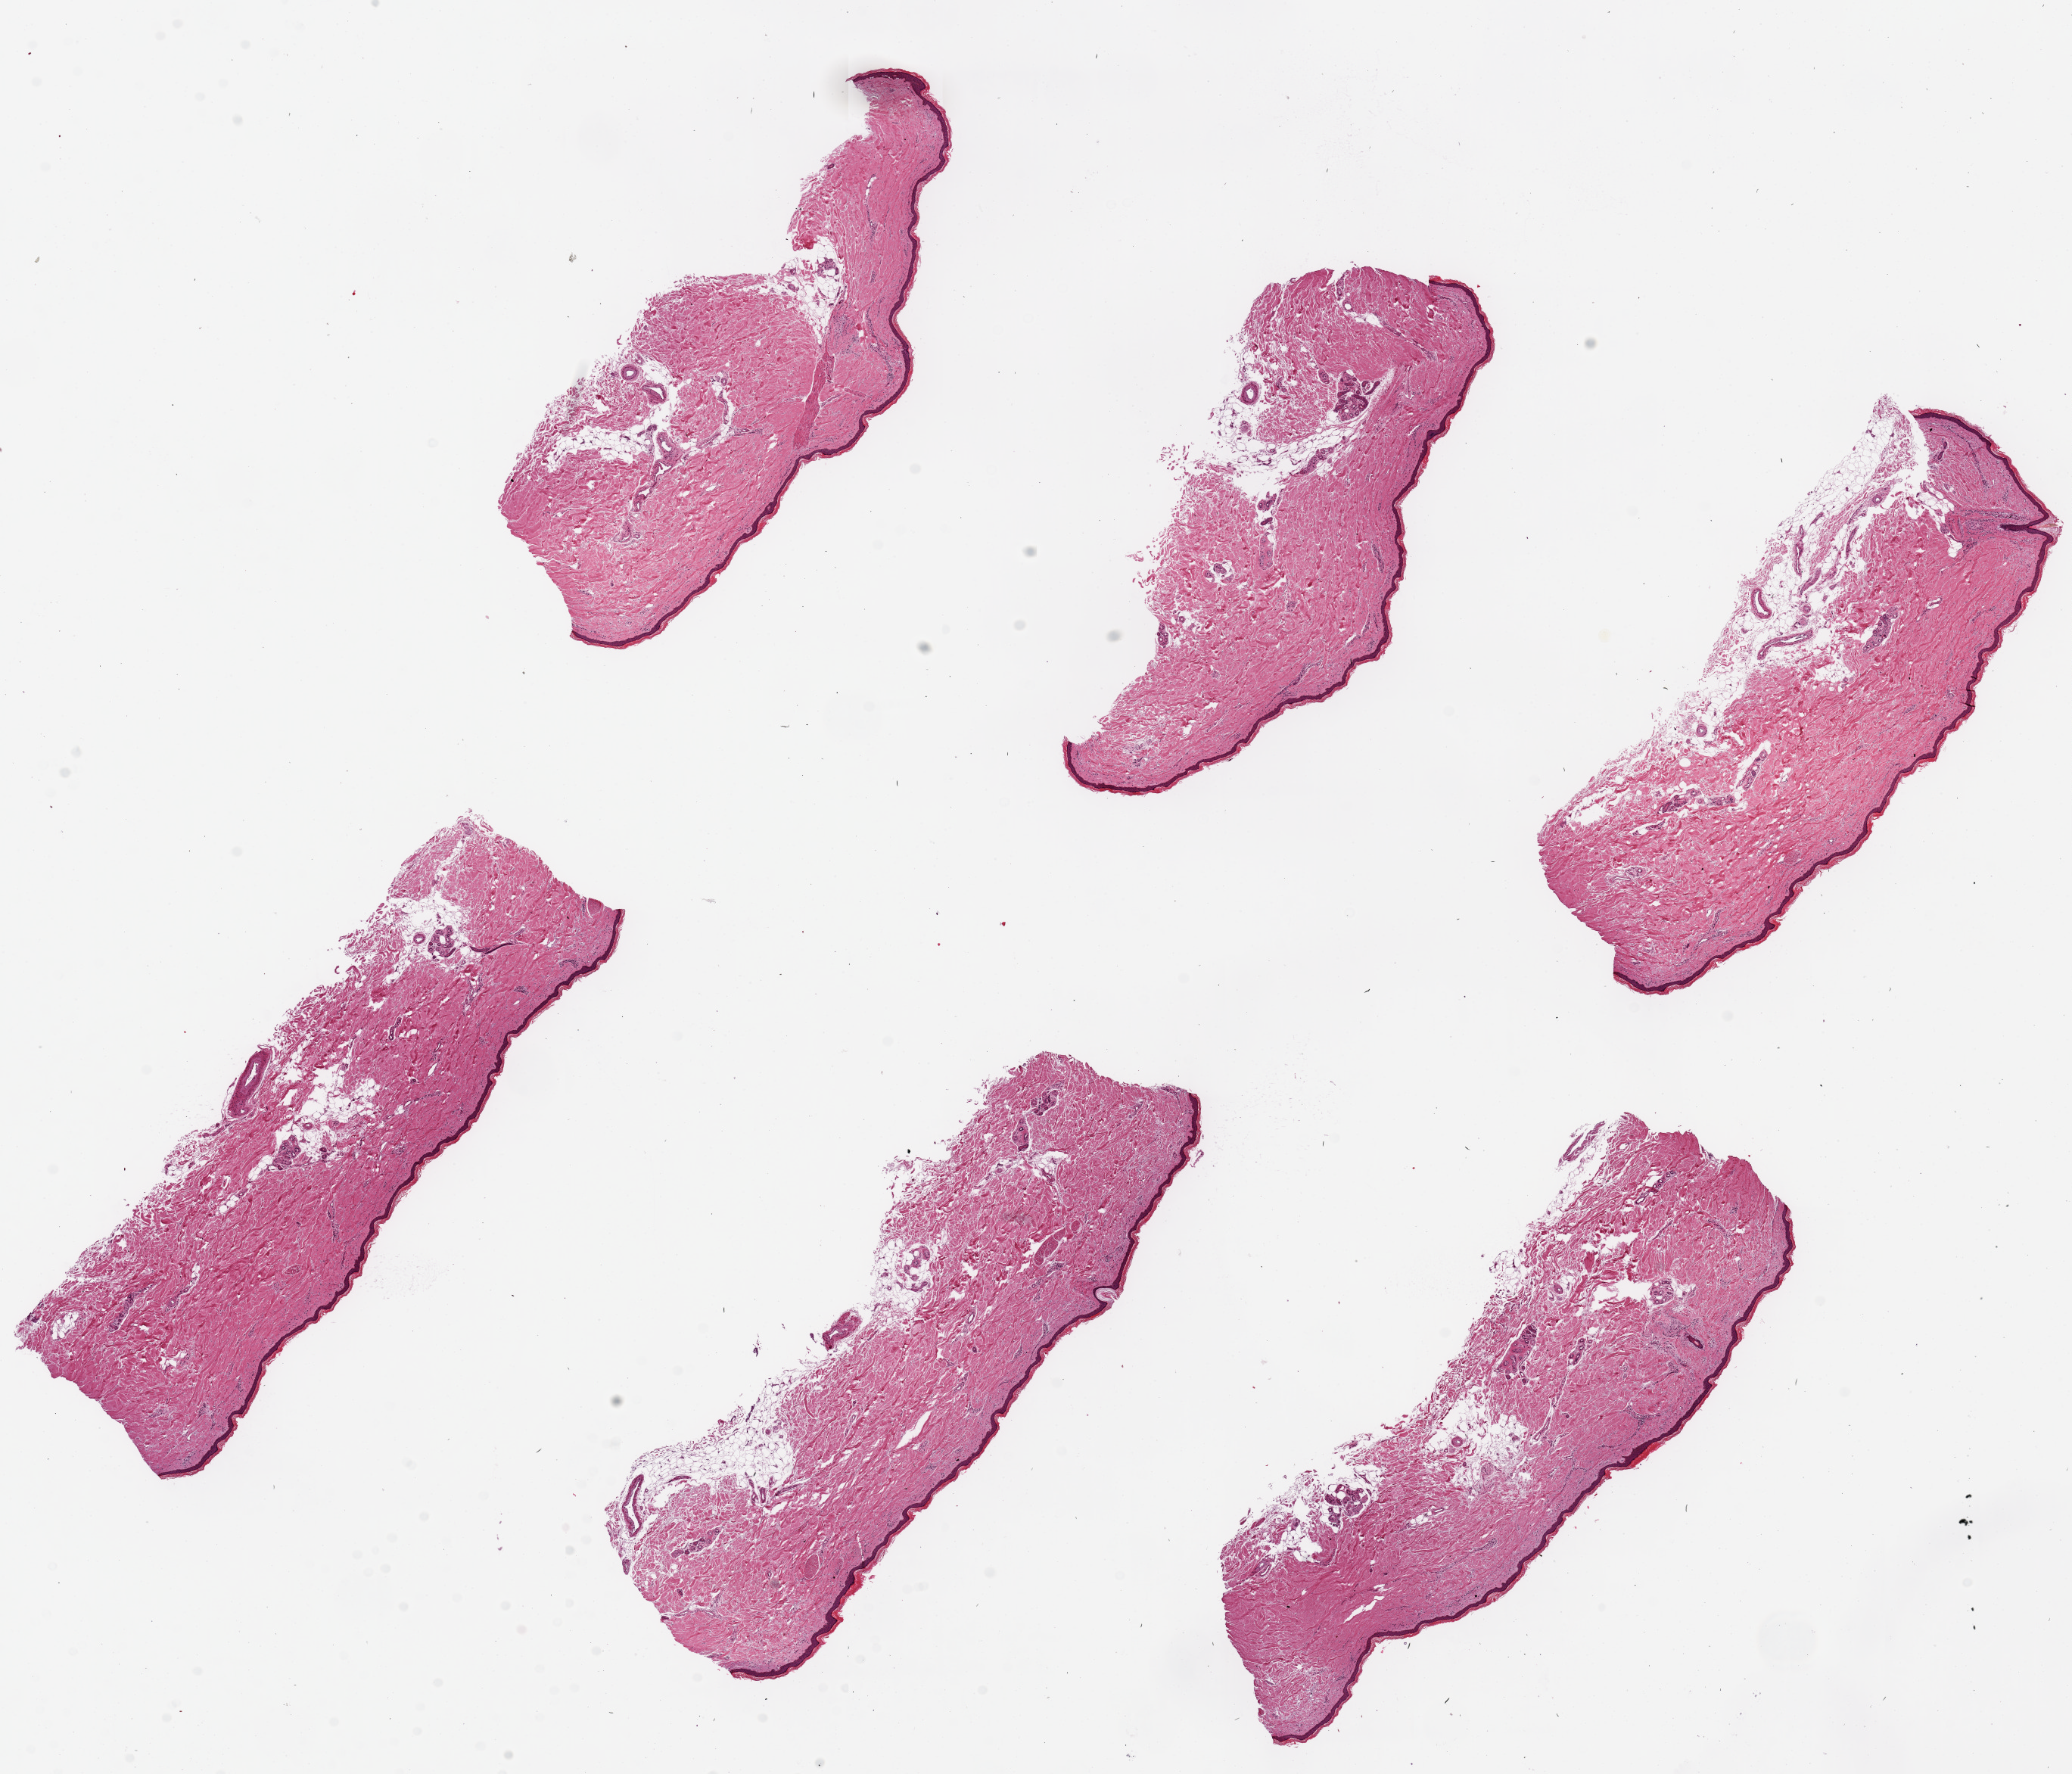
Whole-slide image, hematoxylin and eosin (H&E) stain — a low-resolution overview of the entire scanned area, about 21.7 x 18.5 mm; PAXgene-fixed, paraffin-embedded tissue; sampled site (target tissue): skin of lower leg; donor tissue sample. Donor: male.
Reviewer comment on this tissue sample: 6 pieces ~7x2.5mm; squamous epithelium is ~2% thickness.